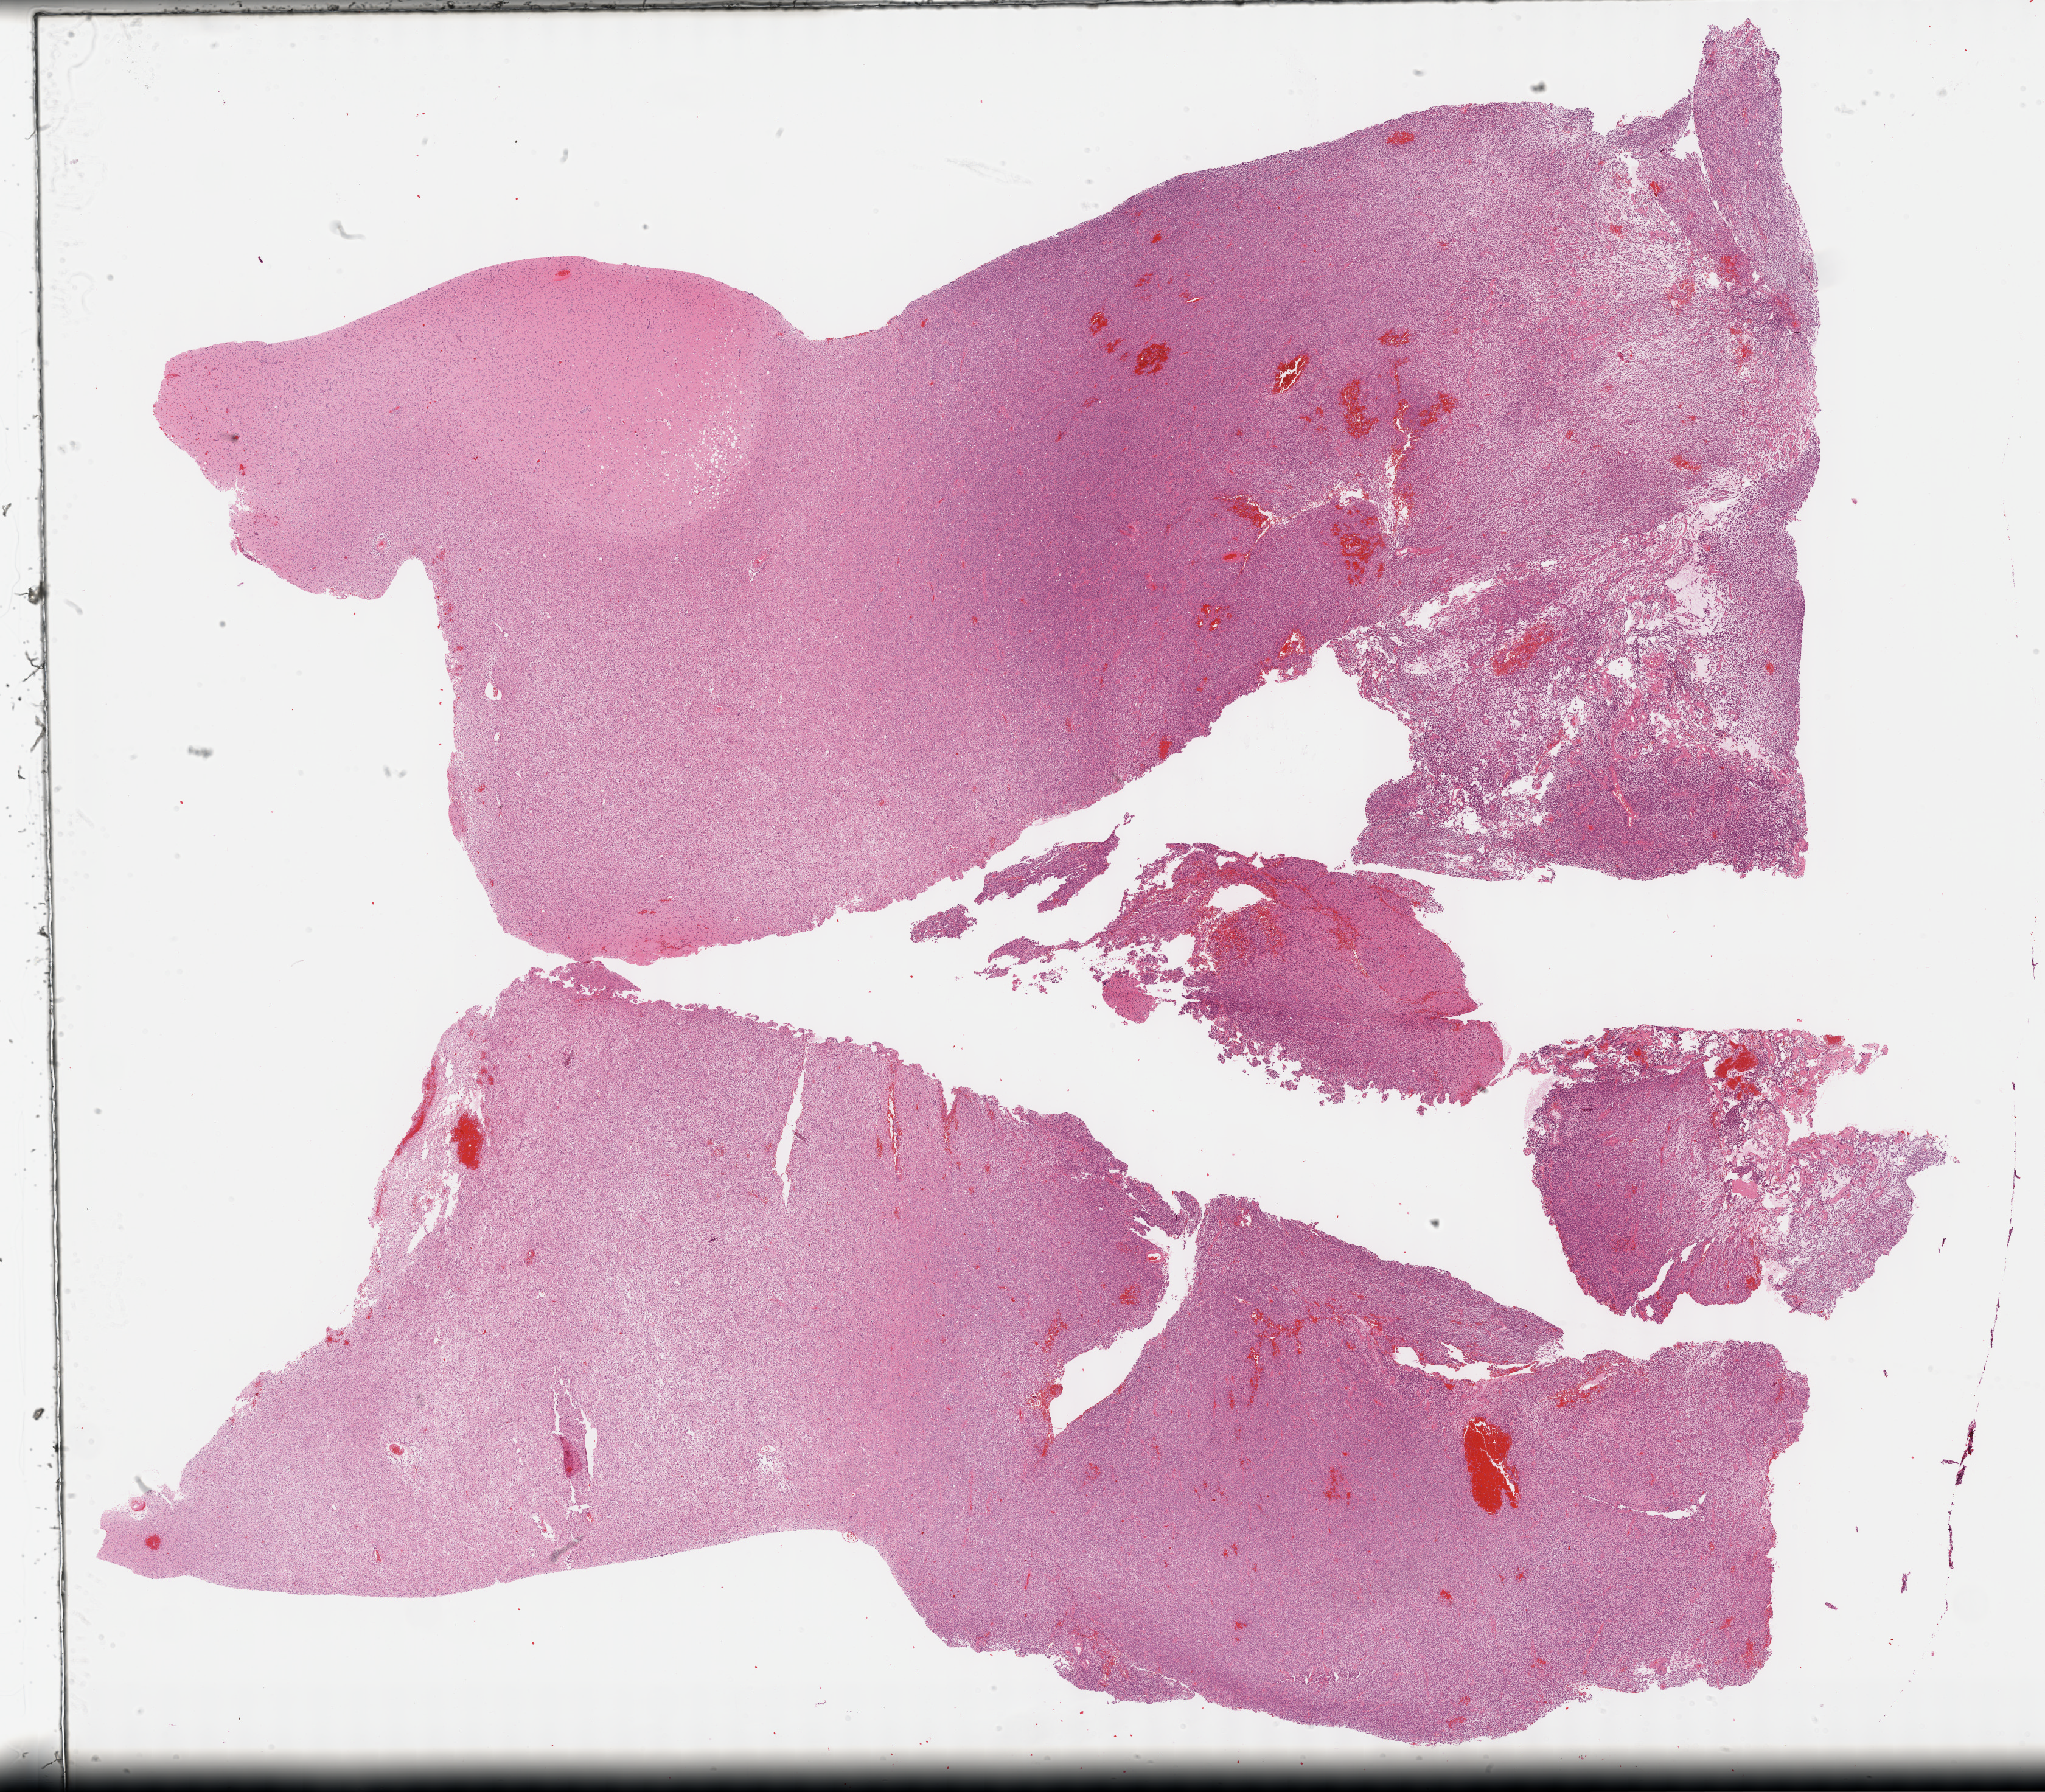
Whole-slide histology image, H&E-stained, a low-resolution overview of the entire scanned area, about 27.2 x 23.8 mm (from a 40x scan). FFPE section. Sample: primary tumour, brain. Patient: female, age at initial diagnosis 30 years. Histologic grade: G3 (poorly differentiated).
* diagnosis: Oligodendroglioma, anaplastic (cerebrum)
* laterality: right